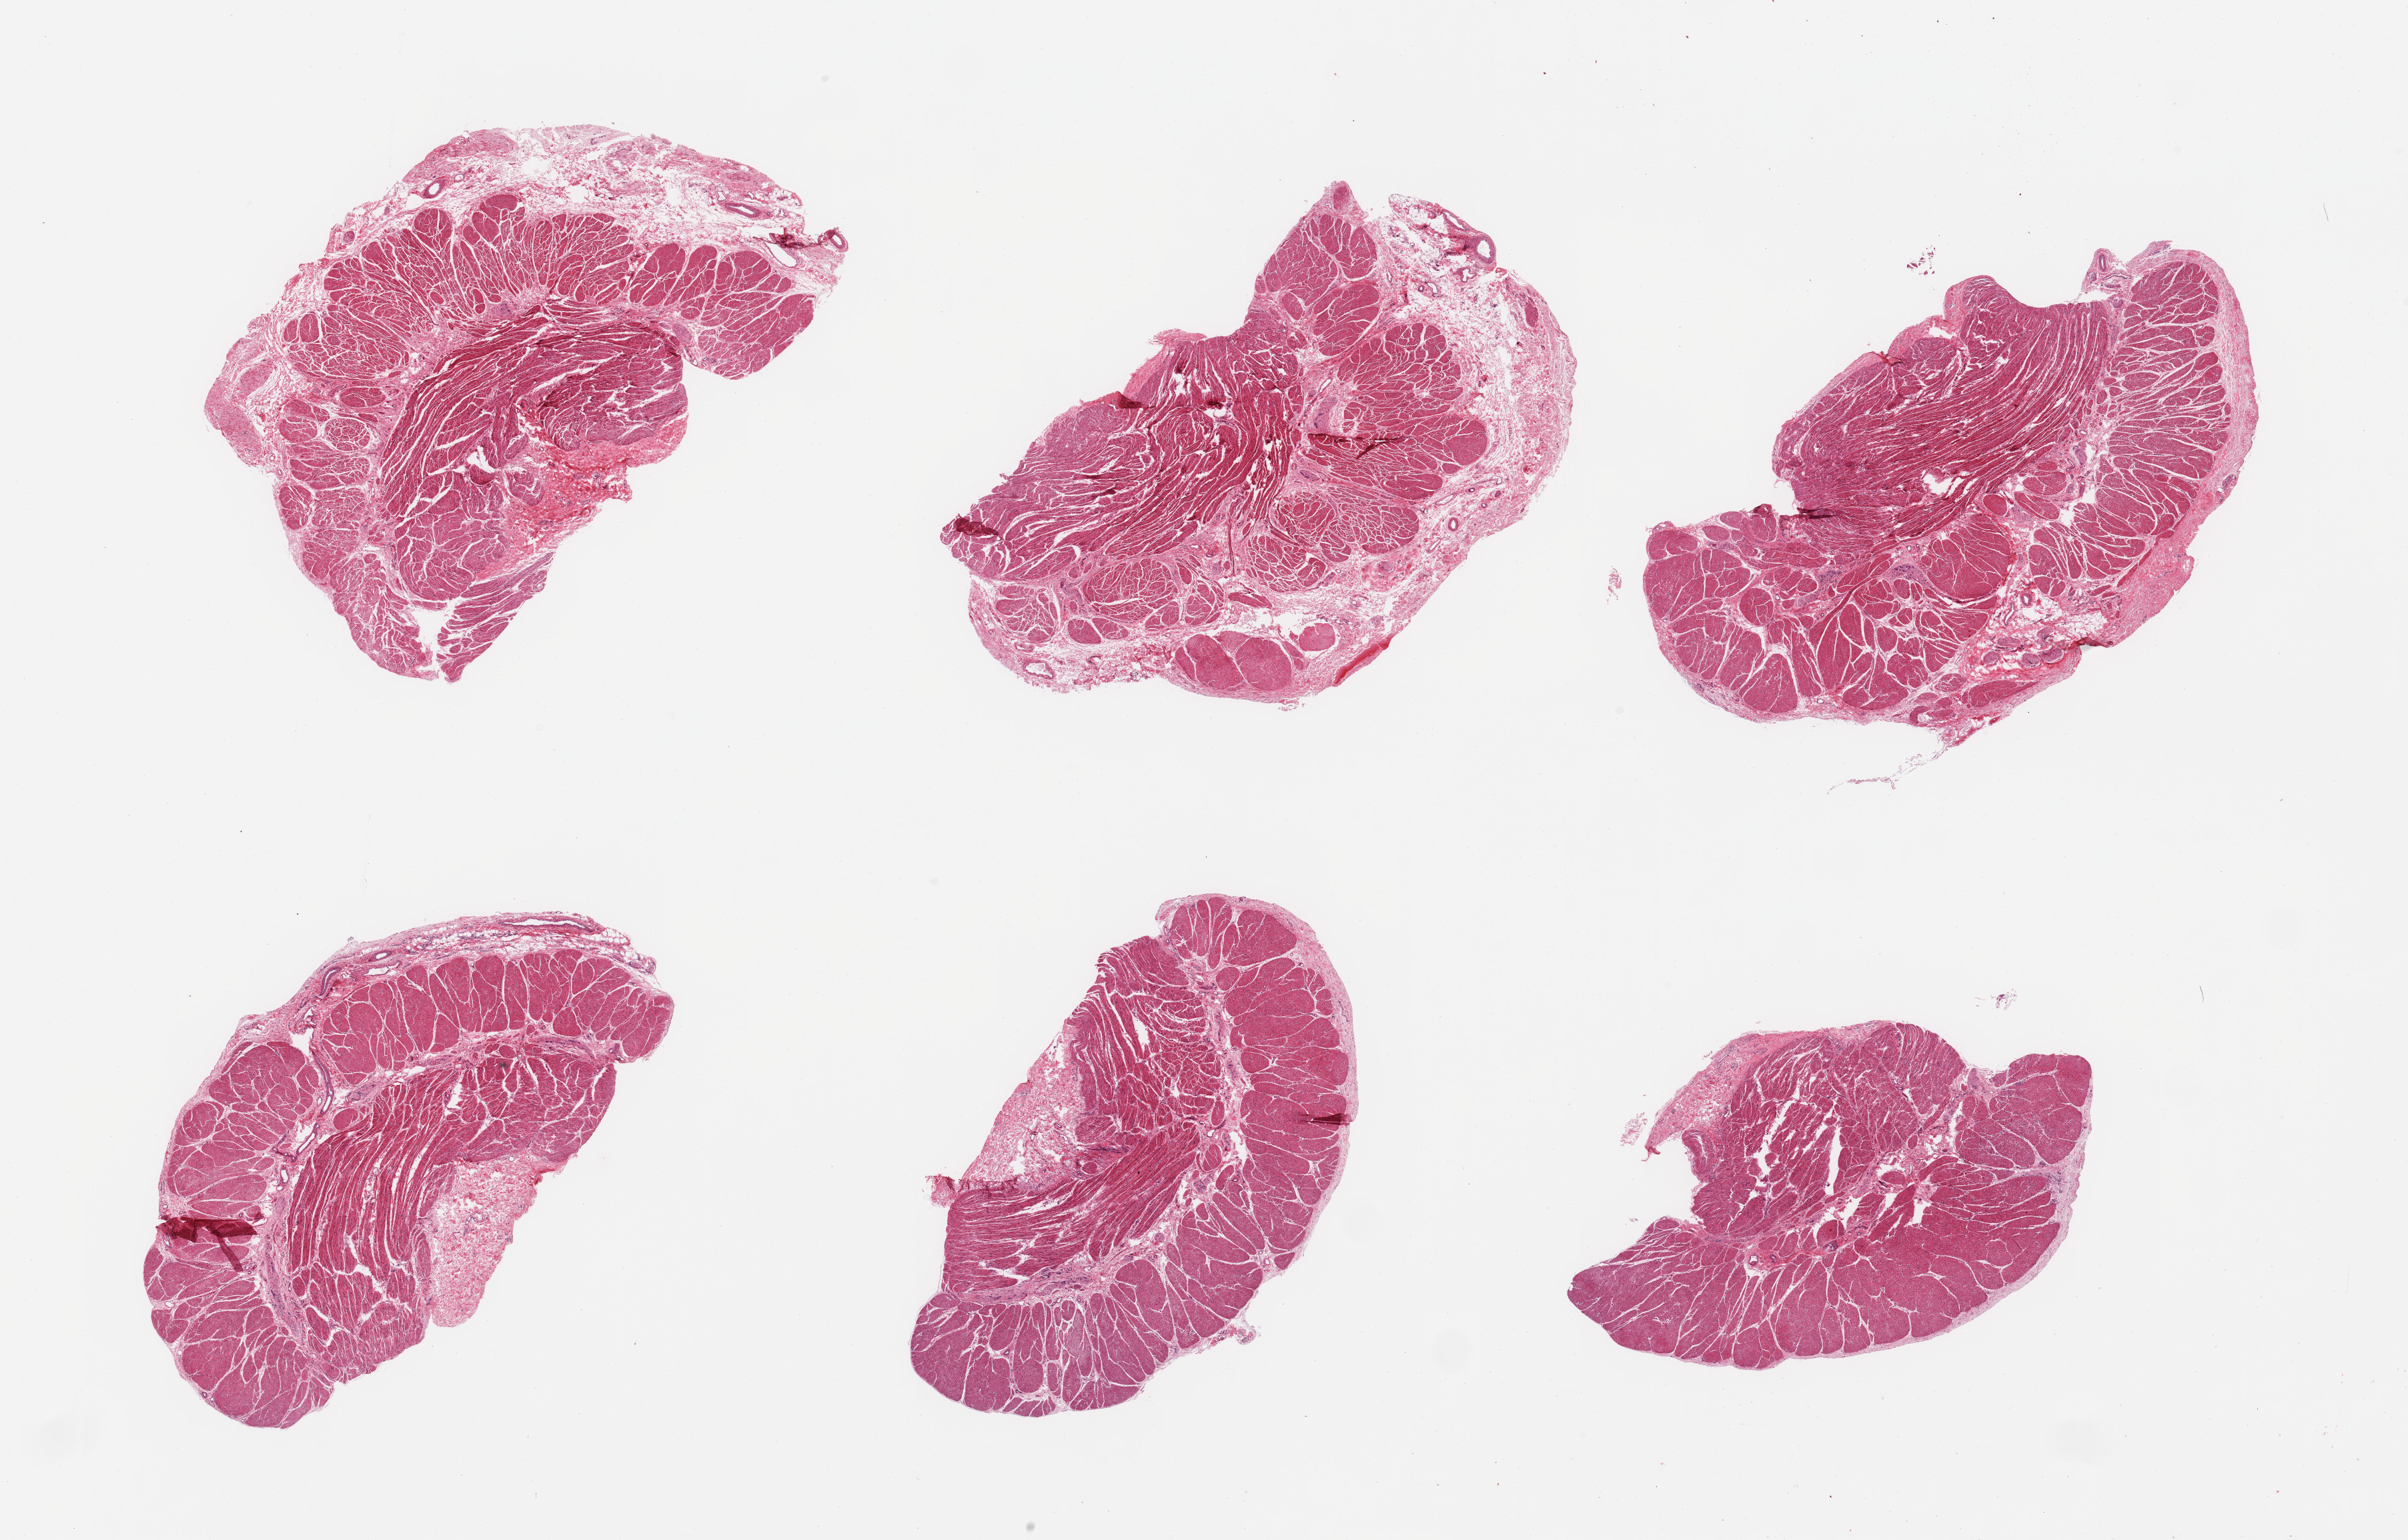
Hematoxylin and eosin (H&E) whole-slide image — shown as a low-resolution overview of the whole scanned area (about 28.5 x 18.3 mm, slide scanned at 20x); PAXgene-fixed paraffin-embedded (PFPE) section; target tissue: gastroesophageal junction; tissue donor sample. Donor sex: male.
* review note (as recorded): 6 pieces; target muscularis